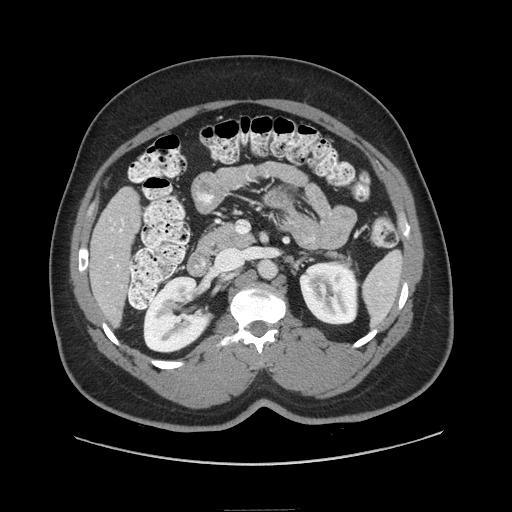
Contrast-enhanced abdominal CT (liver protocol), one axial slice; slice 27 of 87 in the series (ordered by position); reconstruction kernel STANDARD; 140 kVp; soft-tissue window (W 400 / L 40 HU); 512 × 512 image matrix, field of view 440 × 440 mm. From the clinical record (not read from this slice): diagnosis: hepatocellular carcinoma (patient treated with transarterial chemoembolisation; whether this scan precedes or follows treatment is not stated here); TNM stage (as recorded): Stage-II; Child-Pugh class: A; tumour differentiation: moderately differentiated; tumour nodularity: uninodular.
Outlined on this slice (semi-automatically segmented with operator editing):
- liver parenchyma outside the tumour (the mass and vessels are separate outlines, so this box may not span the whole liver): box from (x=90, y=186) to (x=140, y=324) px
- liver vessels: (x=110, y=219)–(x=124, y=287)